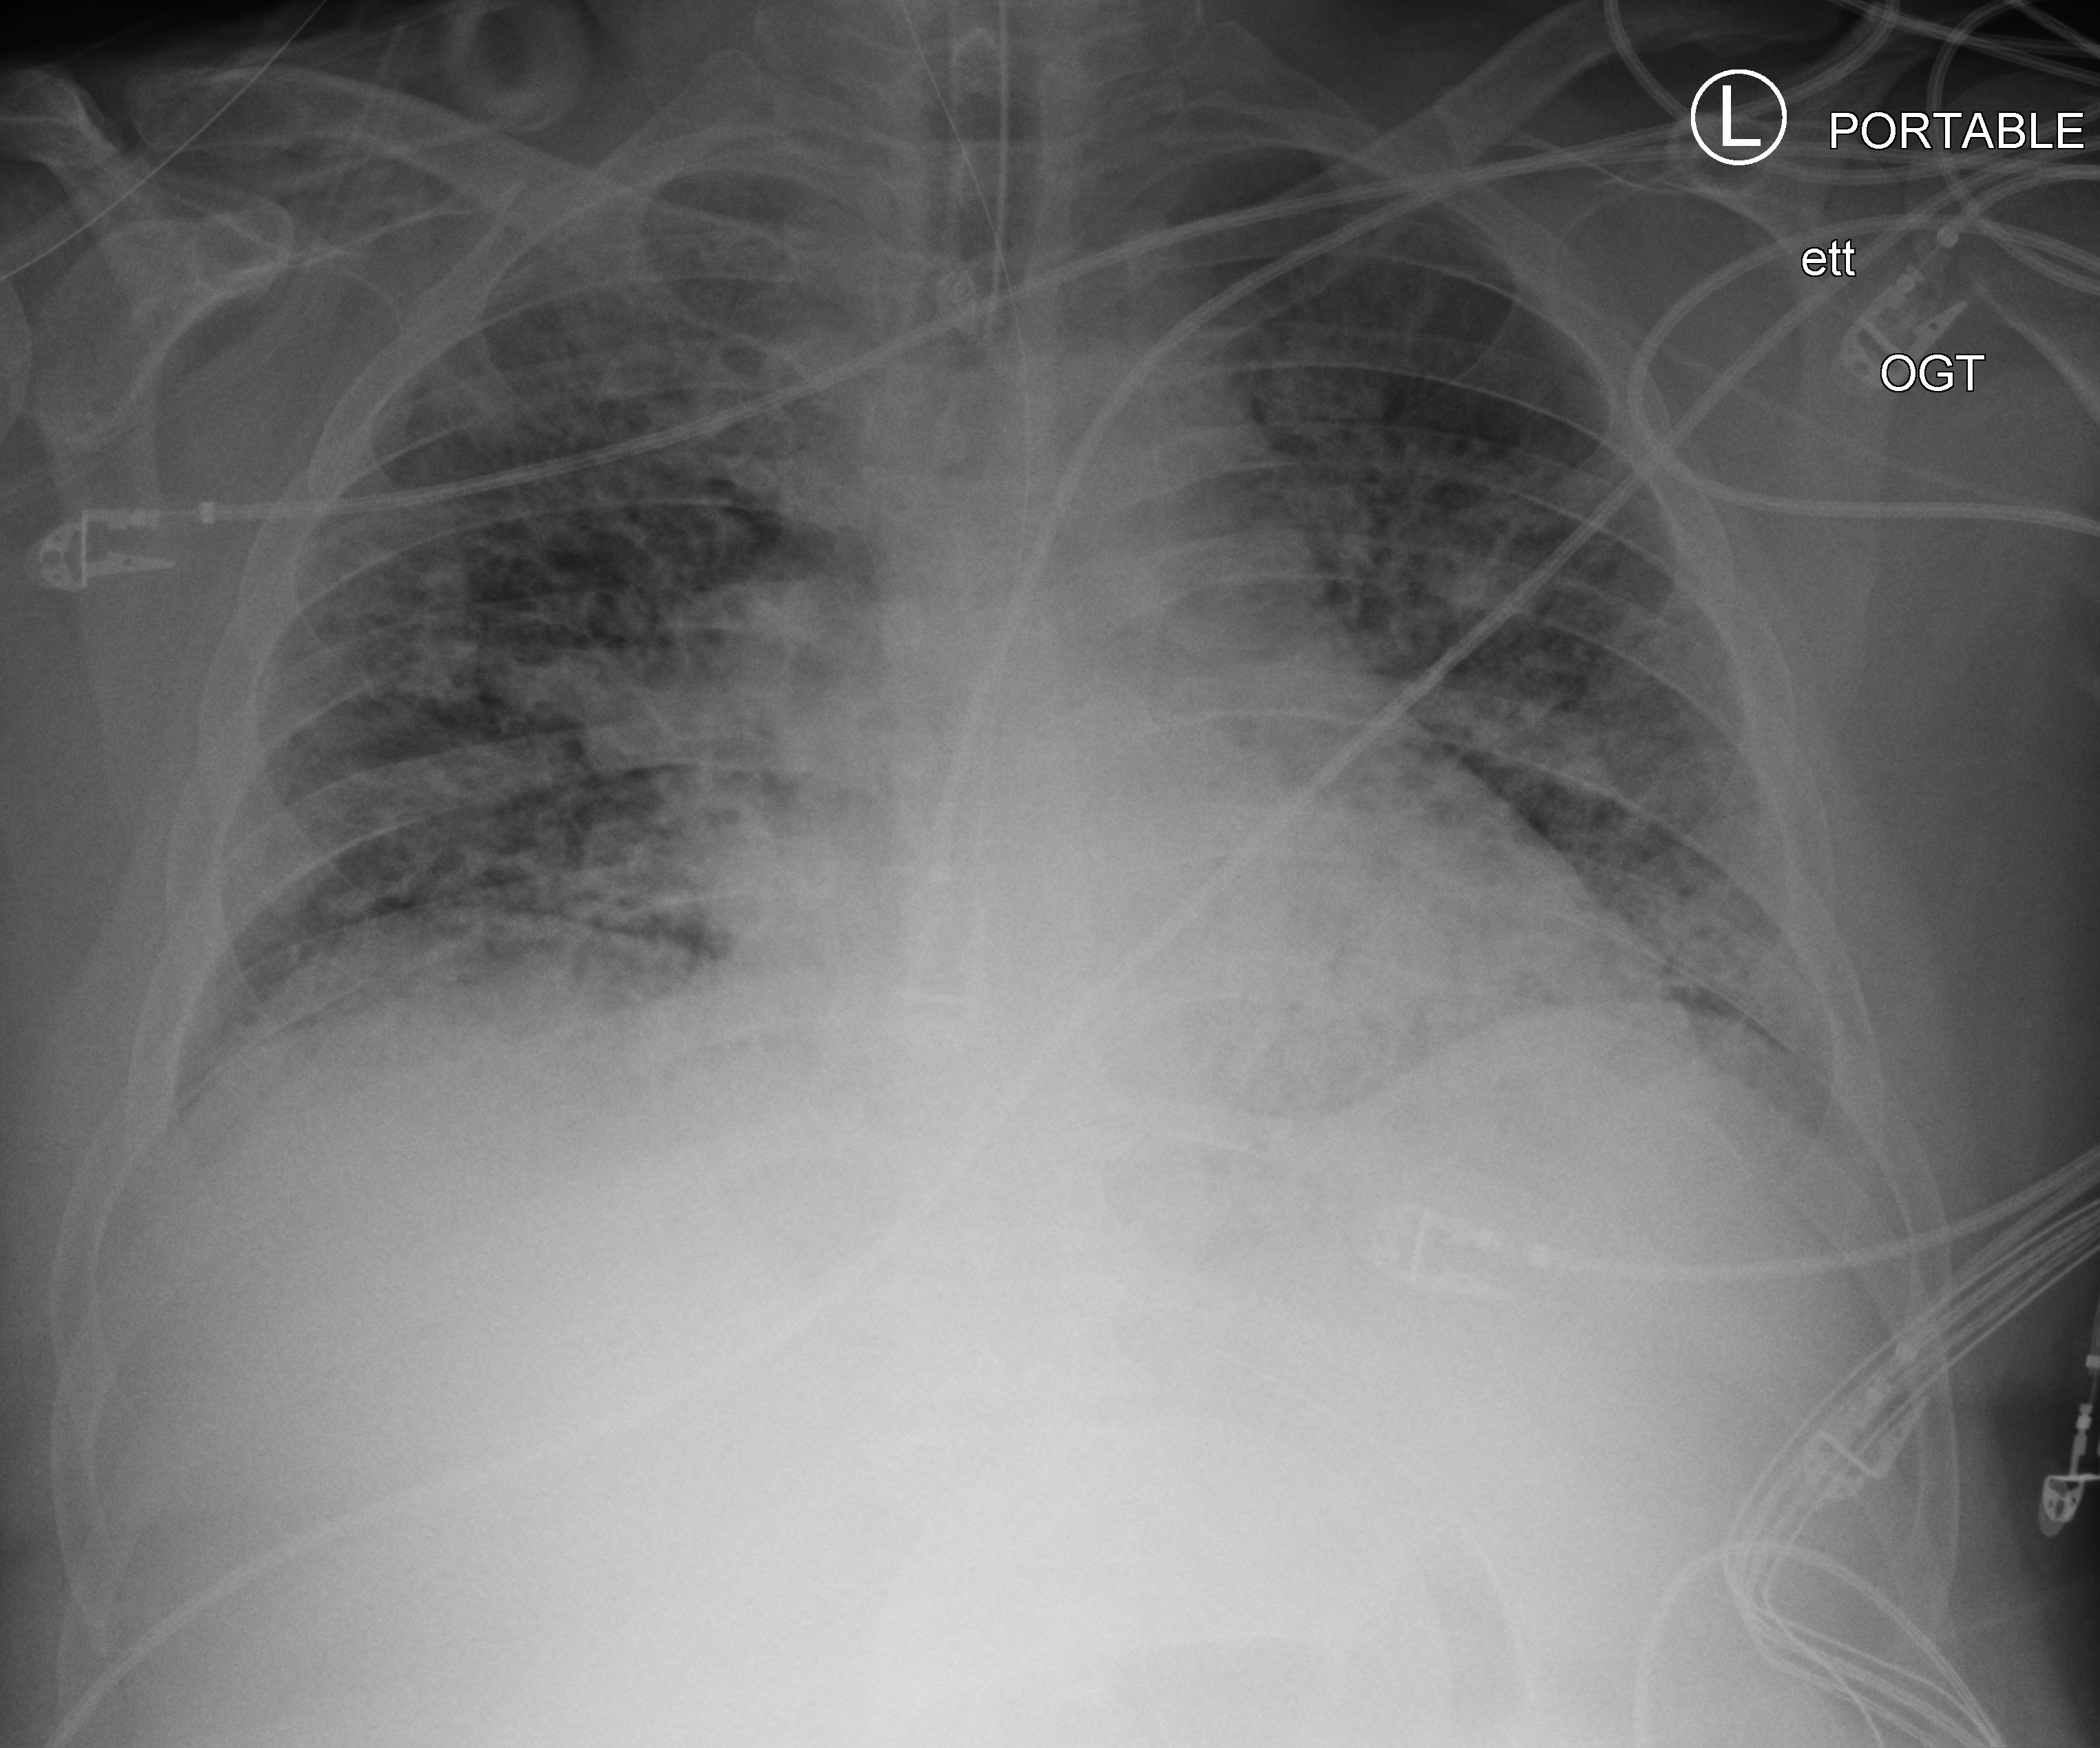
Portable chest radiograph, anteroposterior (AP) projection. Adult patient hospitalised with COVID-19, age 18–59 years.
From the hospital-stay record, not from the radiograph (when in the stay this image was taken is not recorded): admitted to intensive care during this hospital stay: yes.